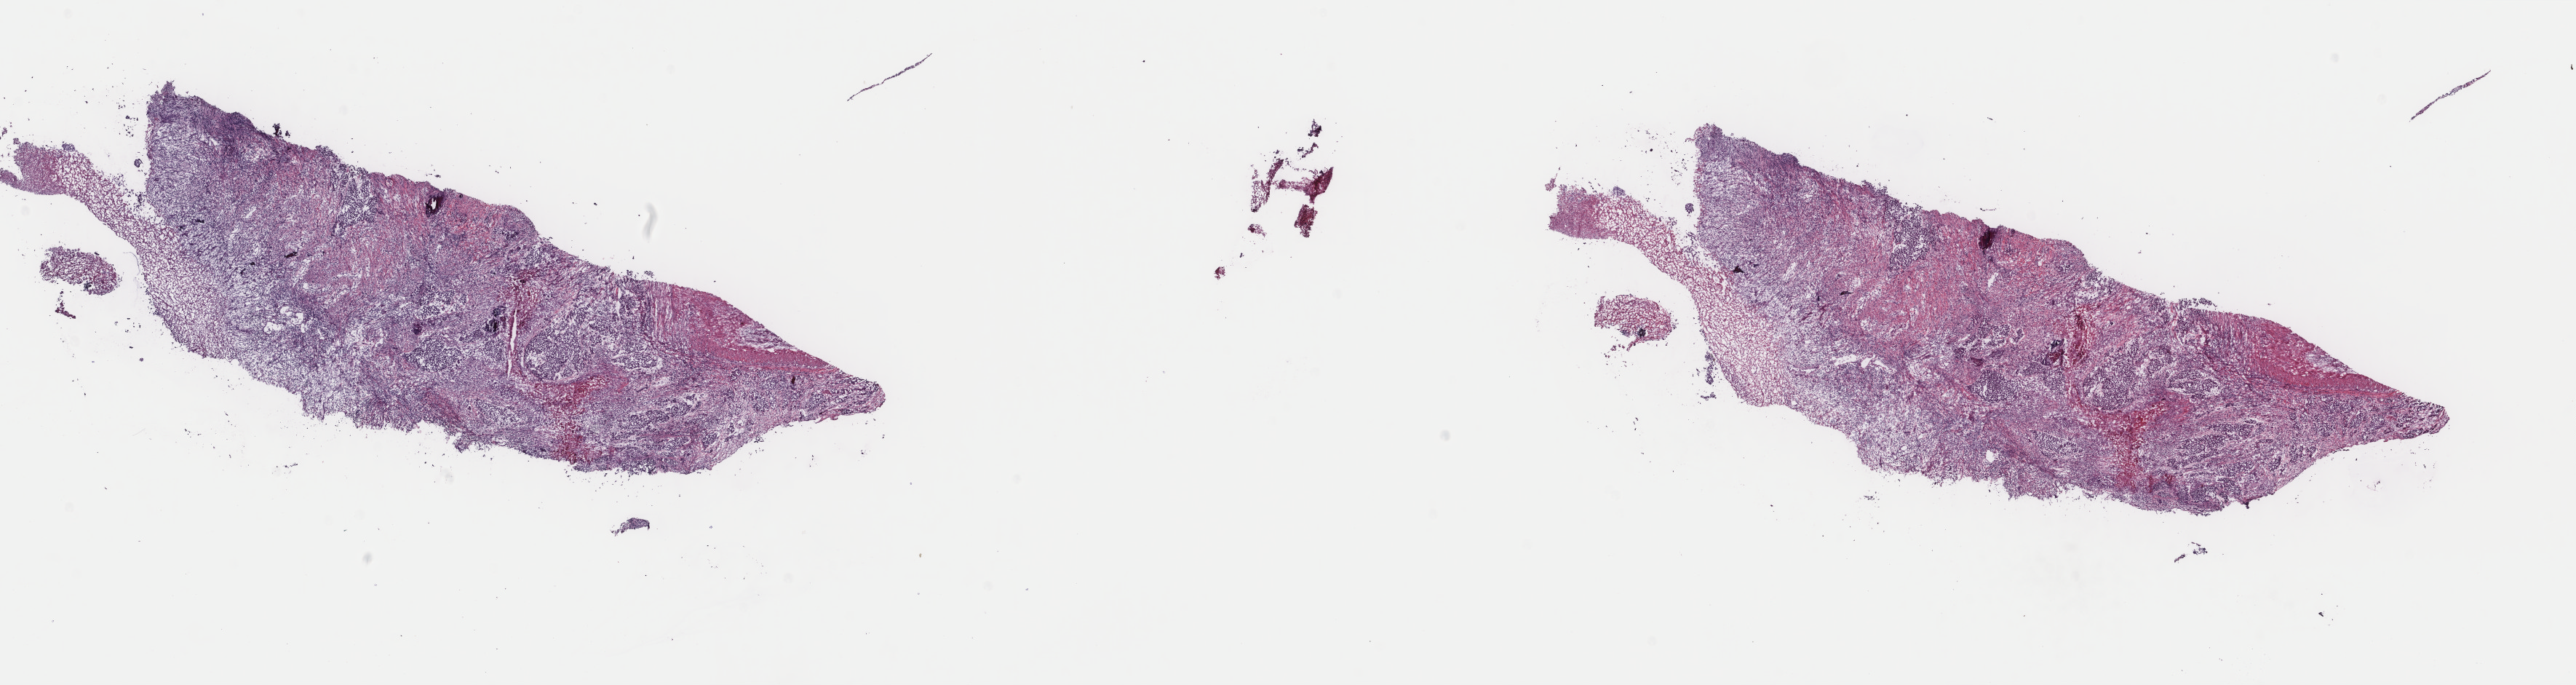
Whole-slide histology image, H&E, whole scanned area (about 28.1 x 7.5 mm) shown as a low-resolution overview. Frozen section from the top of the tissue portion. Sample: primary tumour, bladder. Patient: male, age at initial diagnosis 70 years. Histologic grade: high grade. Pathologist review of this section (percent, as recorded): tumour cells 80%, tumour nuclei 80%, normal cells 0%, stromal cells 10%, necrosis 10%. Inflammatory infiltration, as recorded: lymphocyte infiltration 0%, monocyte infiltration 0%, neutrophil infiltration 0%.
AJCC pathologic stage: IV (7th edition). TNM: T4a N2 MX. Histologic diagnosis: Transitional cell carcinoma (lateral wall of bladder). Lymph nodes positive (case pathology): 7 of 34 examined.